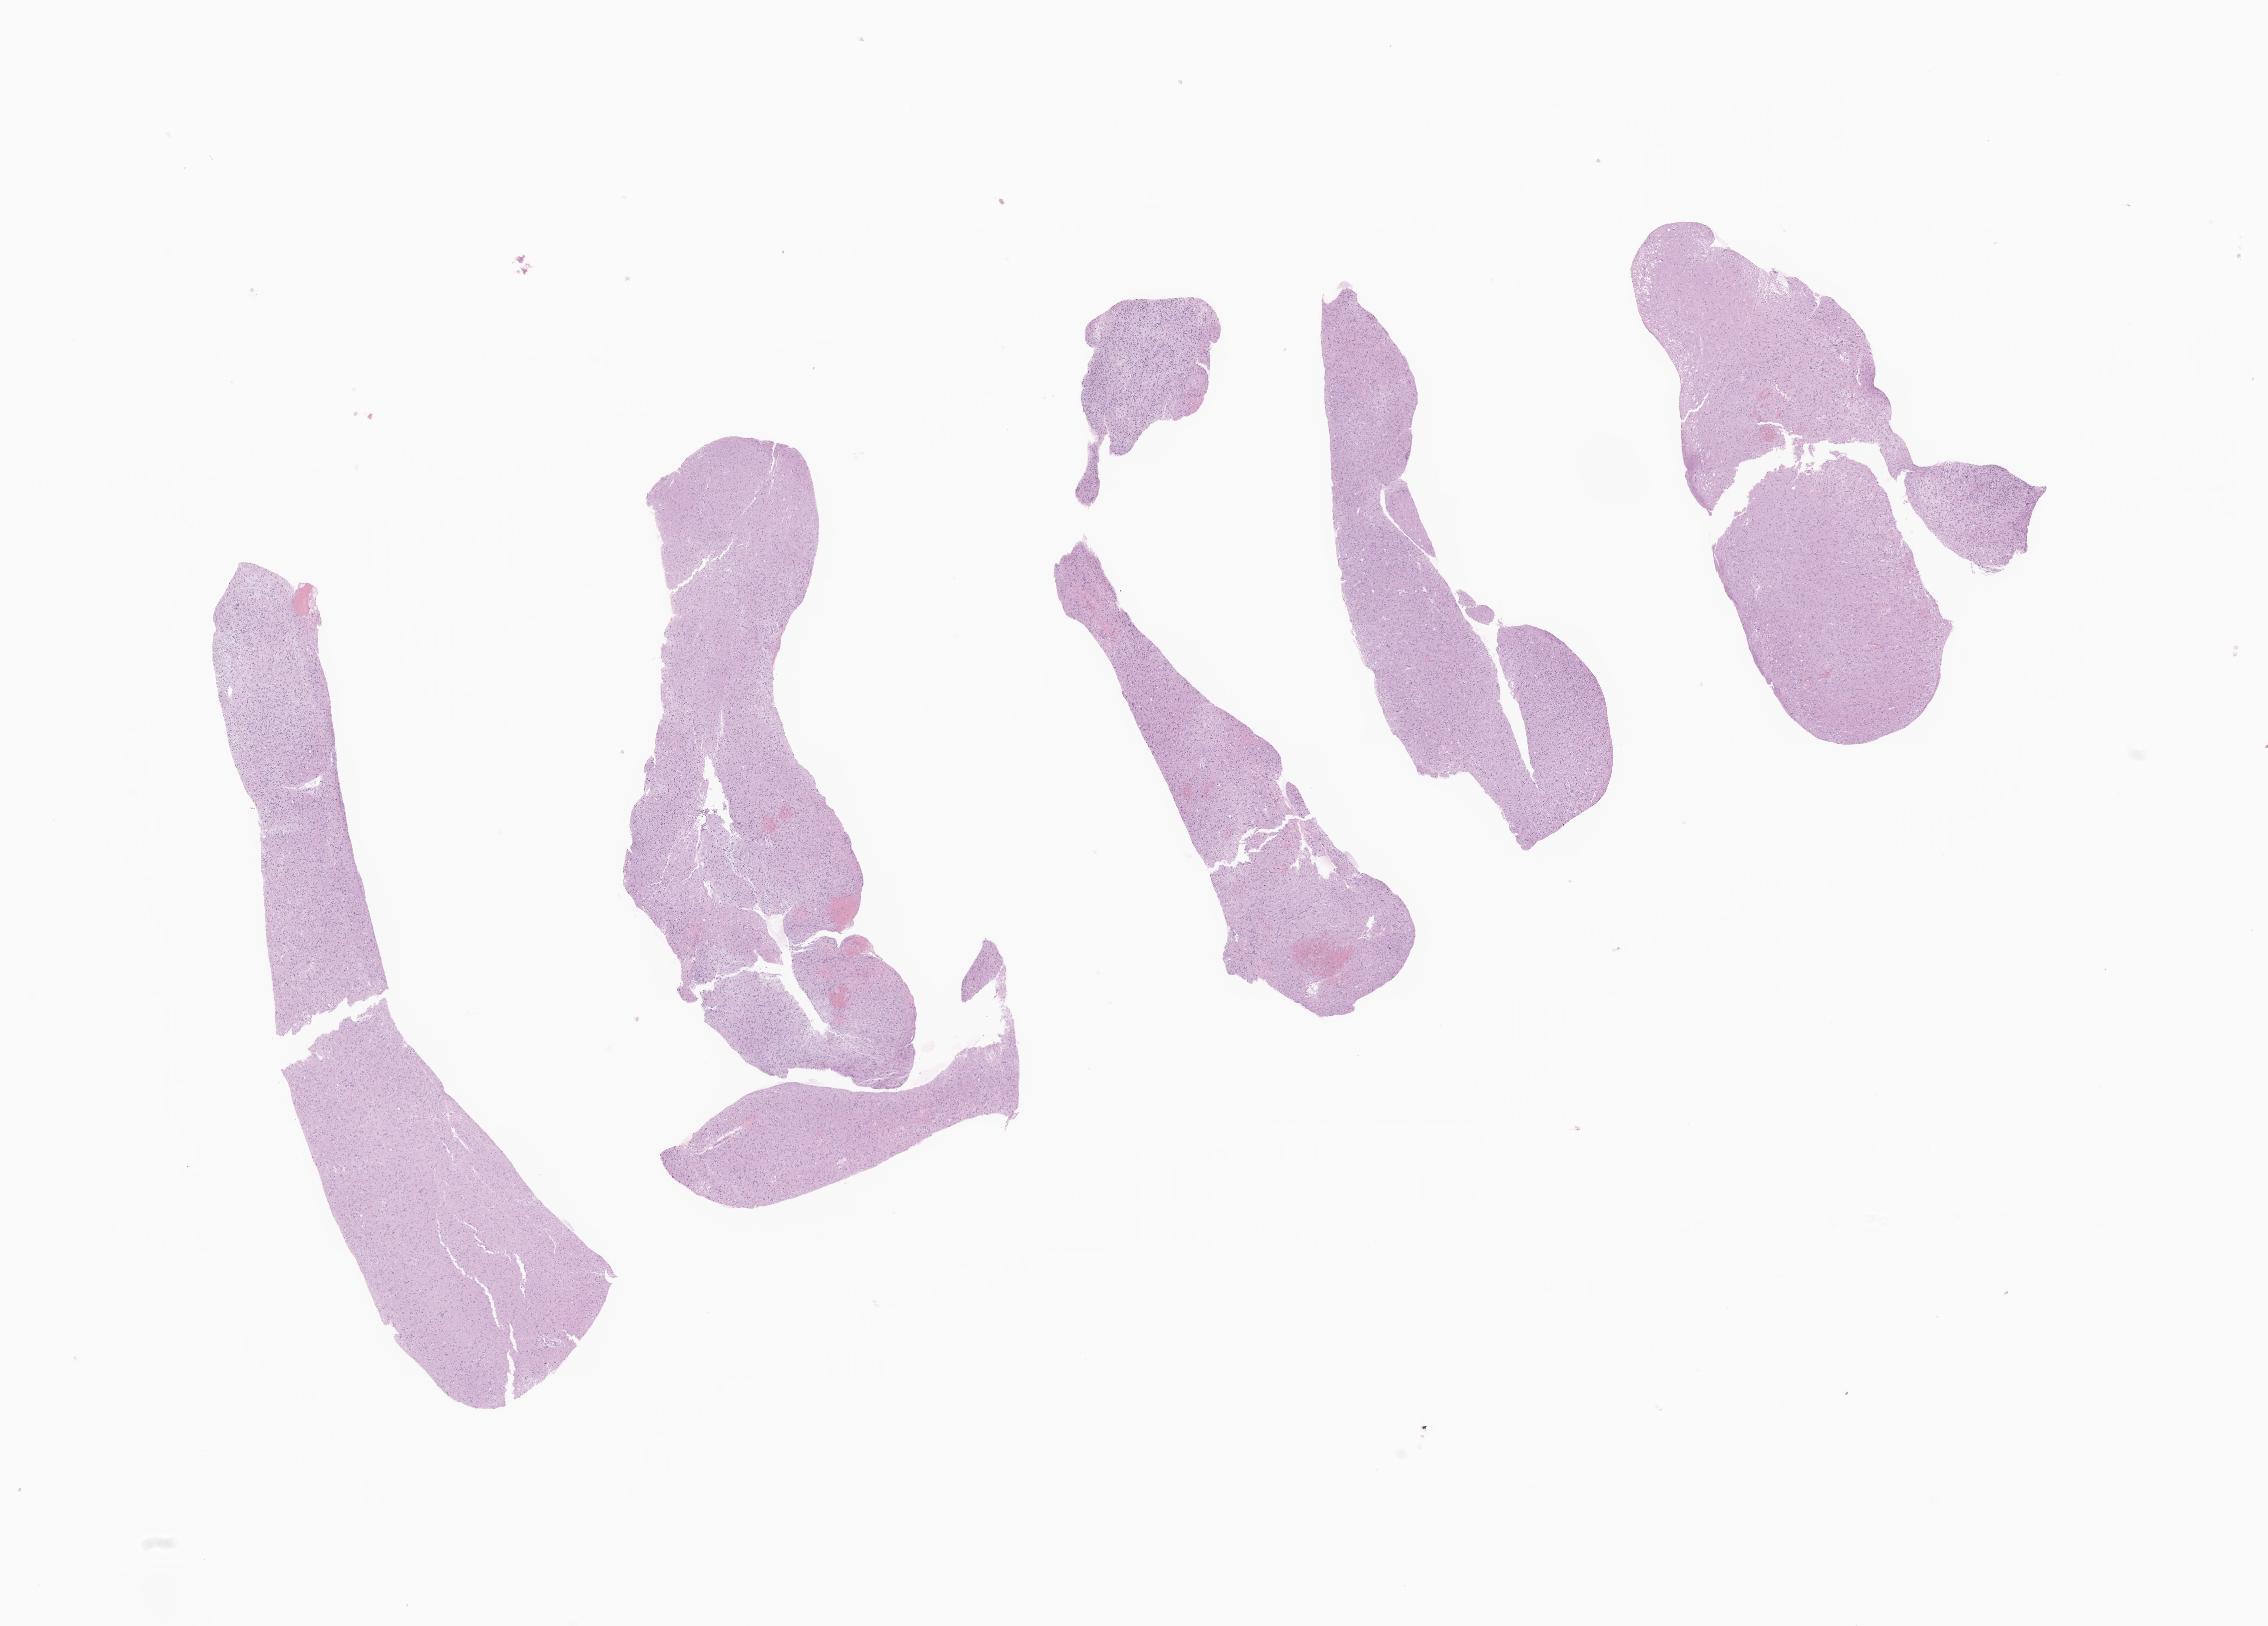
Hematoxylin and eosin (H&E) whole-slide image of tumor tissue from the brain stem, shown as a low-resolution overview of the whole scanned area (about 19.1 x 13.7 mm). Formalin-fixed paraffin-embedded section. Patient: female, age 64 months (5 years 4 months).
Recorded diagnosis: Neoplasm, uncertain whether benign or malignant.